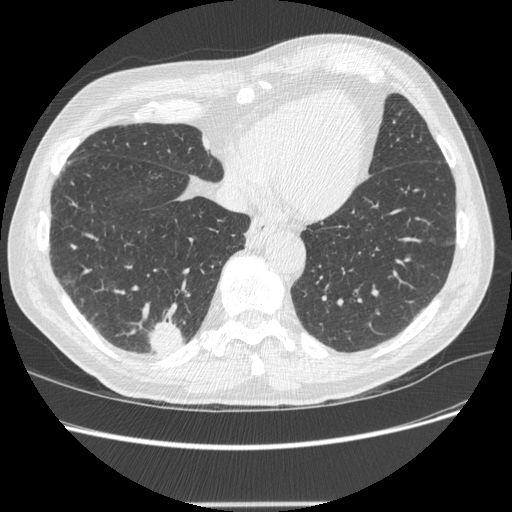
Low-dose screening chest CT, one axial slice; position 66 of 245 along the scan axis; 120 kVp; lung window (W 1500 / L -600 HU); 1.25 mm slice thickness; 512 × 512 image matrix, field of view 372 × 372 mm.
Structures marked on this image (manually delineated by an expert):
- lesion 1 (tumor, lower lobe of right lung): bounding box (x1, y1, x2, y2) in pixels: (148, 320, 184, 354)